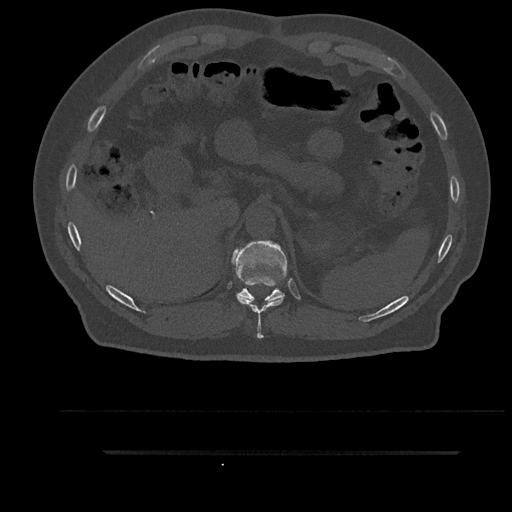
CT including the spine, one axial slice. Position 334 of 797 along the scan axis. Reconstruction kernel Br40s/3. 120 kVp. Bone window (W 1800 / L 400 HU). 0.5 mm slice thickness. 512 × 512 image matrix, field of view 432 × 432 mm. Patient: male, 63 years. From the clinical record (not read from this slice): primary cancer: renal.
Outlined on this slice (semi-automatically segmented with operator editing):
- T10 vertebra: box from (x=236, y=296) to (x=284, y=339) px
- T11 vertebra: (x=232, y=241)–(x=287, y=303)